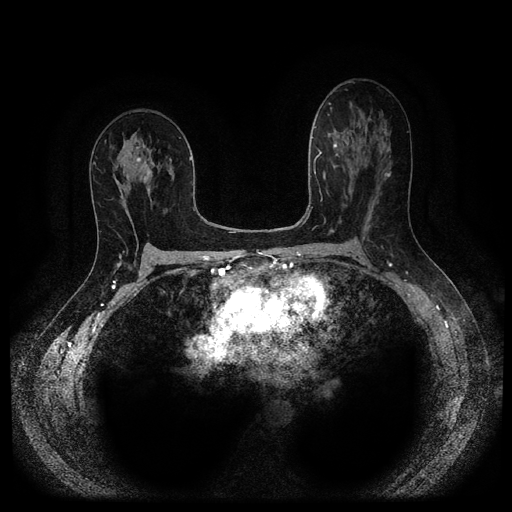
Breast MRI (dynamic contrast-enhanced, multi-phase), one axial slice. Slice 56 of 116 in the series (ordered by position). Dynamic contrast-enhanced series, time point 2 of 5 at this slice position (early post-contrast). 1.5 T. TE 2.6 ms, TR 5.3 ms. 2.2 mm slice thickness. 512 × 512 image matrix, field of view 340 × 340 mm. Patient: female, 50 years.
Annotated regions visible in this slice (semi-automatic segmentation, software-assisted and operator-edited):
- breast lesion (labelled 'tumour' in the annotation; benign lesions carry a separate 'benign' label): bounding box (x1, y1, x2, y2) in pixels: (132, 148, 154, 177)